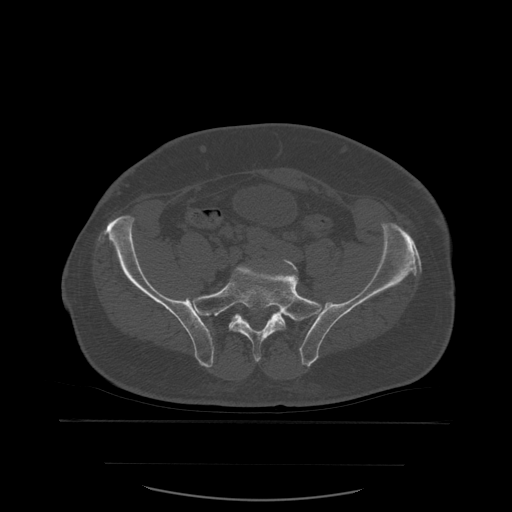
CT including the spine, one axial slice. Slice 115 of 590 in the series (ordered by position). Bone window (W 1800 / L 400 HU). 512 × 512 image matrix. Patient age 71 years. From the clinical record (not read from this slice): primary cancer: lung.
Structures marked on this image (semi-automatic segmentation, software-assisted and operator-edited):
- L5 vertebra: bounding box (x1, y1, x2, y2) in pixels: (255, 260, 299, 358)